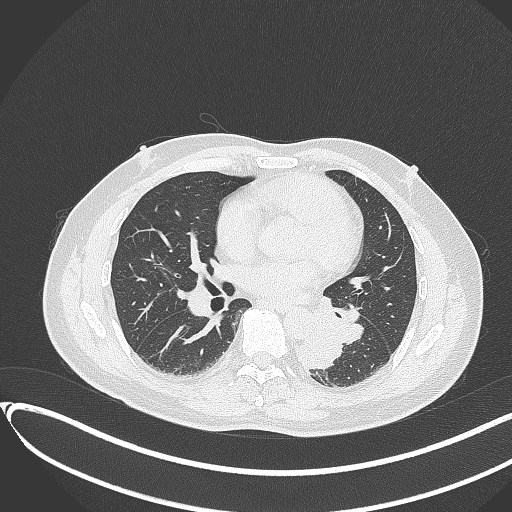
Chest CT, one axial slice; slice 163 of 417 in the series (ordered by position); lung window (W 1500 / L -600 HU); 1 mm slice thickness; 512 × 512 image matrix. Male patient, age 54 years. From the clinical record (not read from this slice): clinical TNM (as recorded): T3 N0 M0.
Outlined on this slice (rectangle marked by the reading radiologist):
- lung tumour (recorded histology: squamous cell carcinoma): bounding box [x1, y1, x2, y2] px = [294, 328, 348, 371]